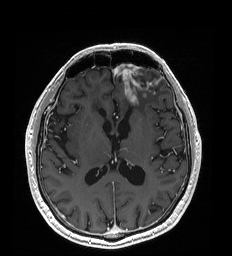
Brain MRI from a brain-tumour surgery series, one axial slice. Position 98 of 192 along the scan axis. T1-weighted post-contrast. 232 × 256 image matrix. Case-level facts recorded for this patient, not image findings: histopathology: Glioblastoma; WHO grade: 4; IDH mutation: no.
Outlined on this slice (expert manual segmentation):
- tumour: bounding box (x1, y1, x2, y2) in pixels: (126, 93, 138, 104)